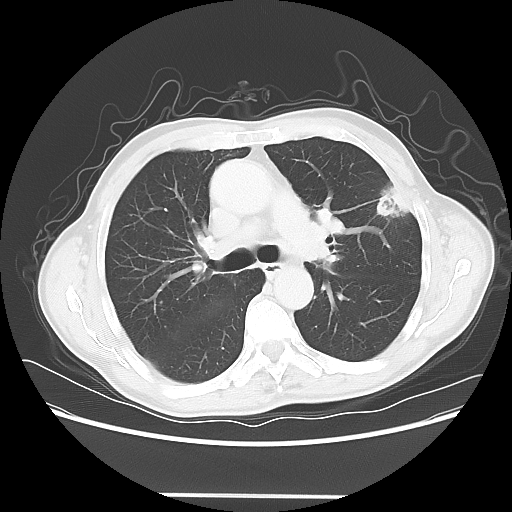
Chest CT, one axial slice; slice 40 of 64 in the series (ordered by position); 120 kVp; lung window (W 1500 / L -600 HU); 5 mm slice thickness; 512 × 512 image matrix. Patient: male, 71 years. From the clinical record (not read from this slice): clinical TNM (as recorded): T1c N0 M0; histopathological grade: G2-3.
Structures marked on this image (rectangle marked by the reading radiologist):
- lung tumour (recorded histology: adenocarcinoma): bounding box (x1, y1, x2, y2) in pixels: (378, 182, 414, 227)